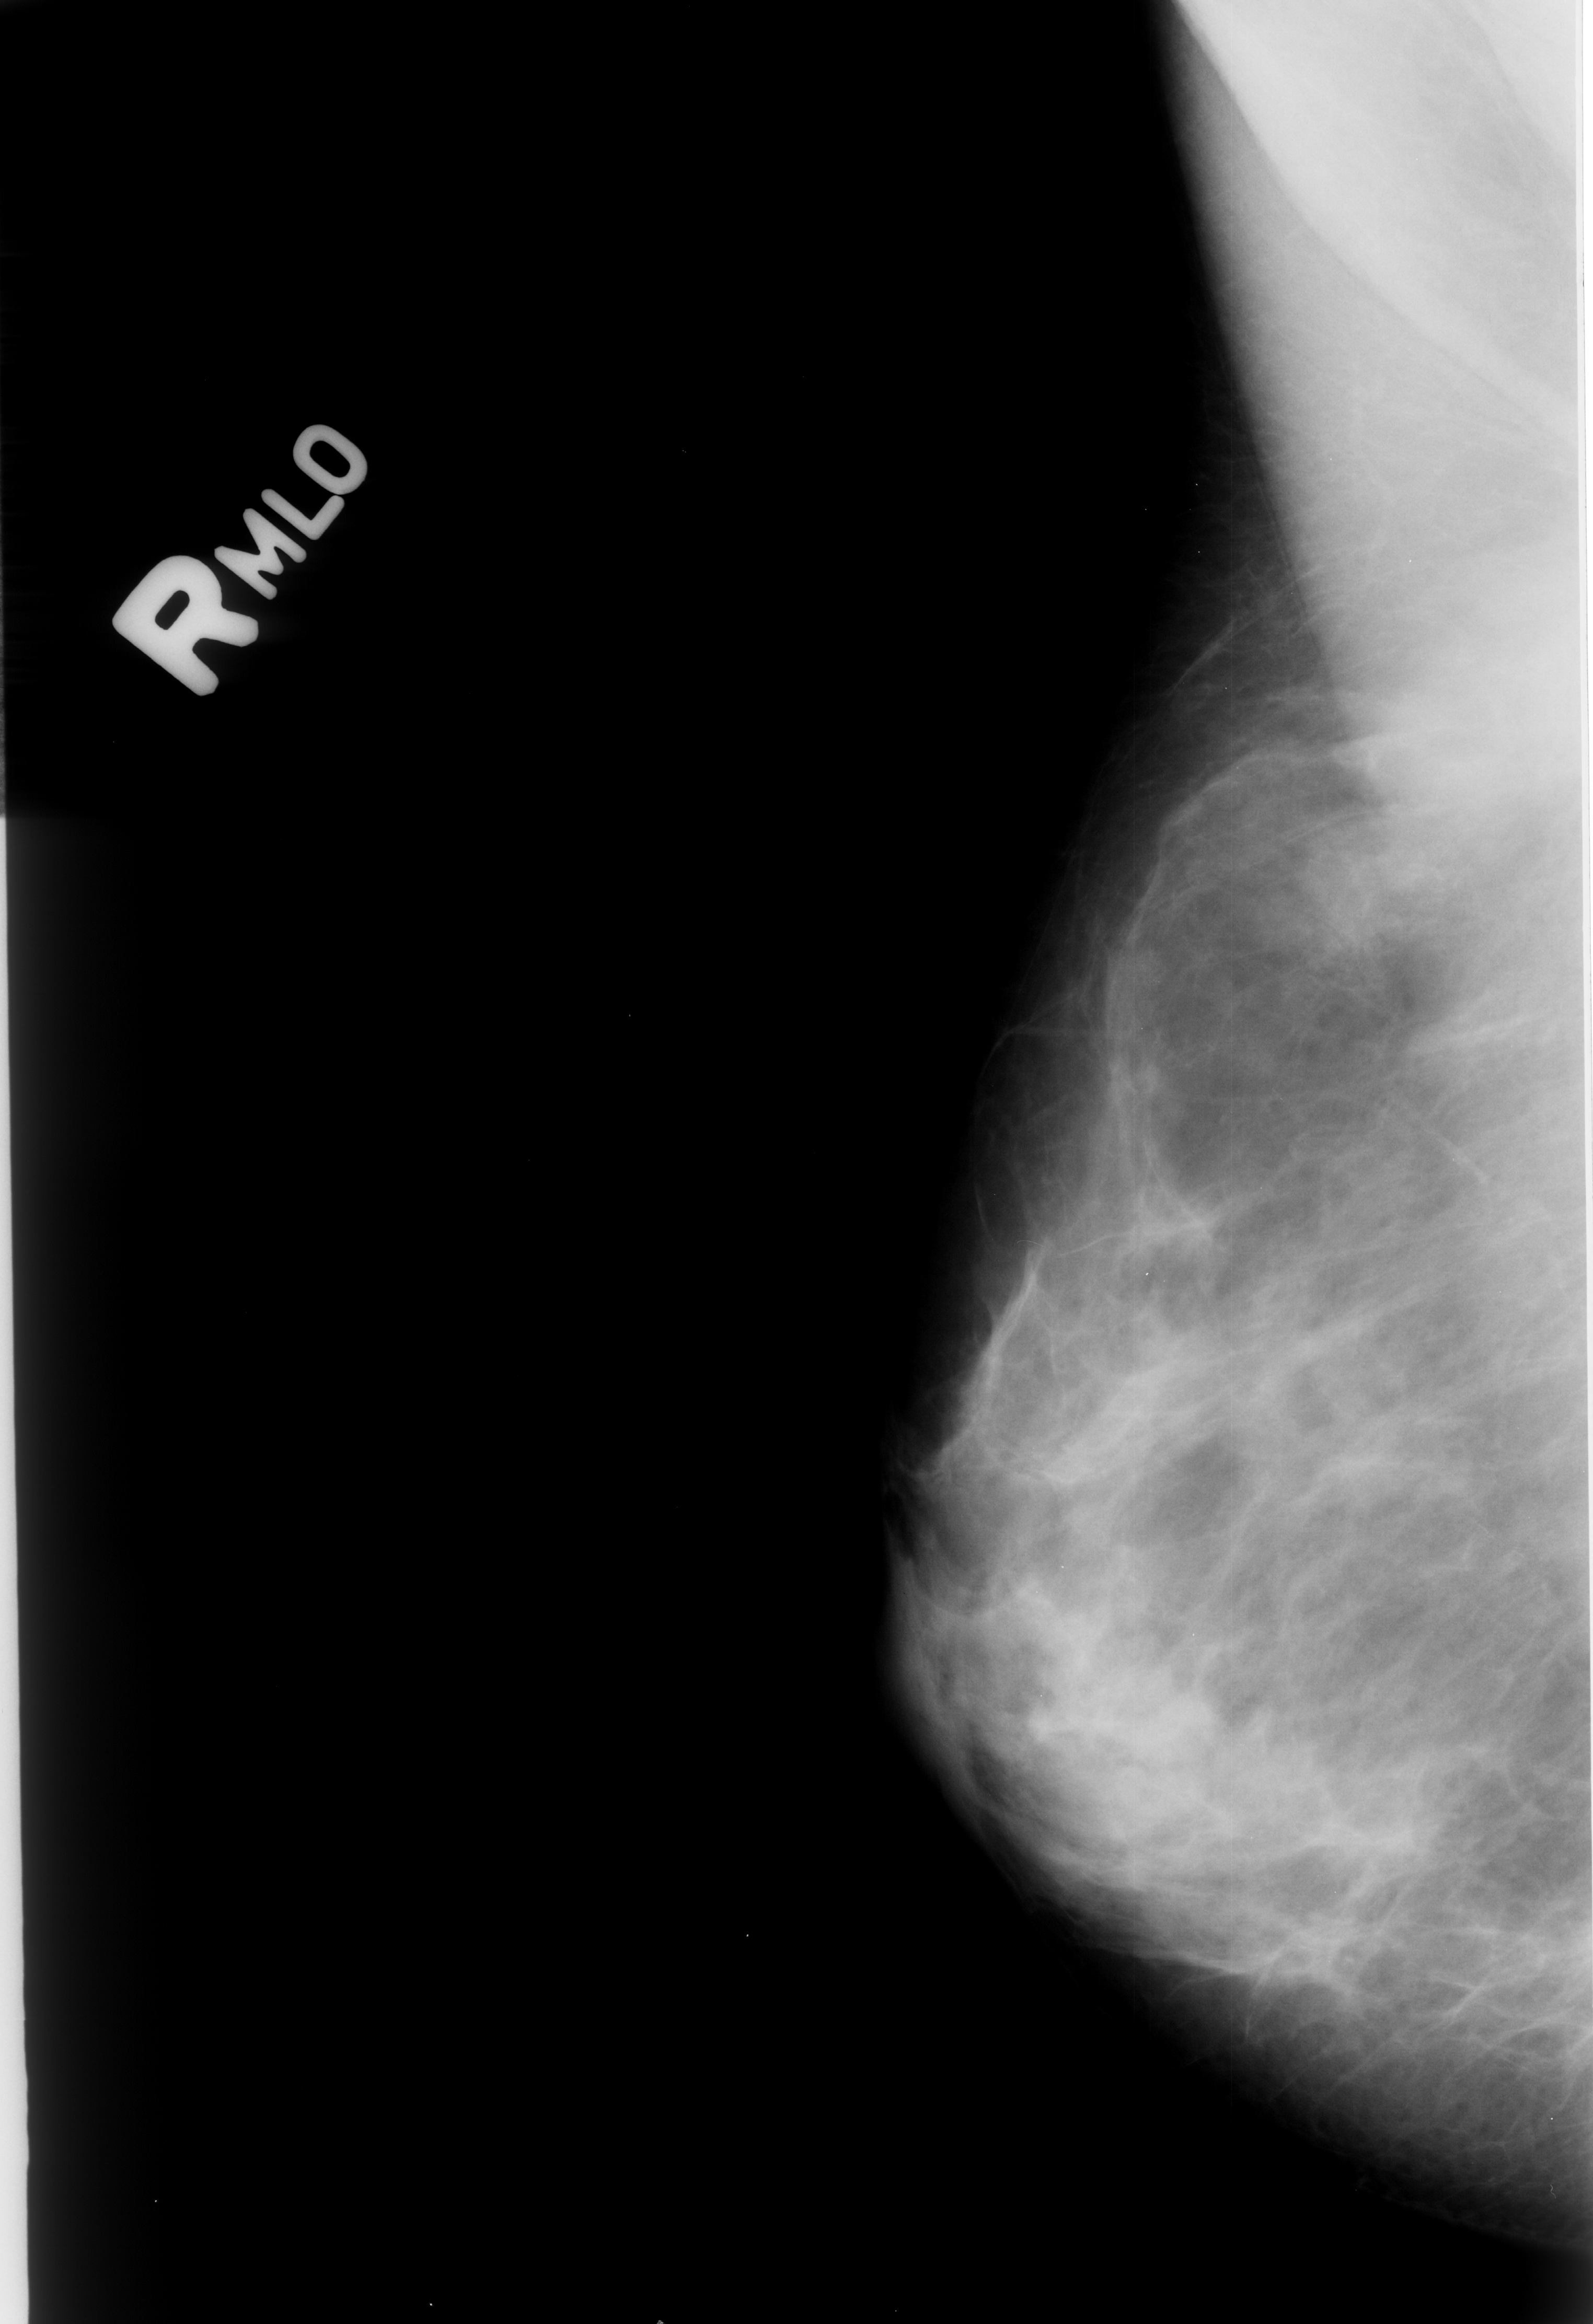
Digitized screen-film mammogram; right breast; MLO view; breast composition: heterogeneously dense (BI-RADS density category 3 of 4).
Radiologist-marked abnormalities on this image: mass, shape focal asymmetric density; BI-RADS assessment category 2; benign; no additional work-up was recommended (benign without callback).